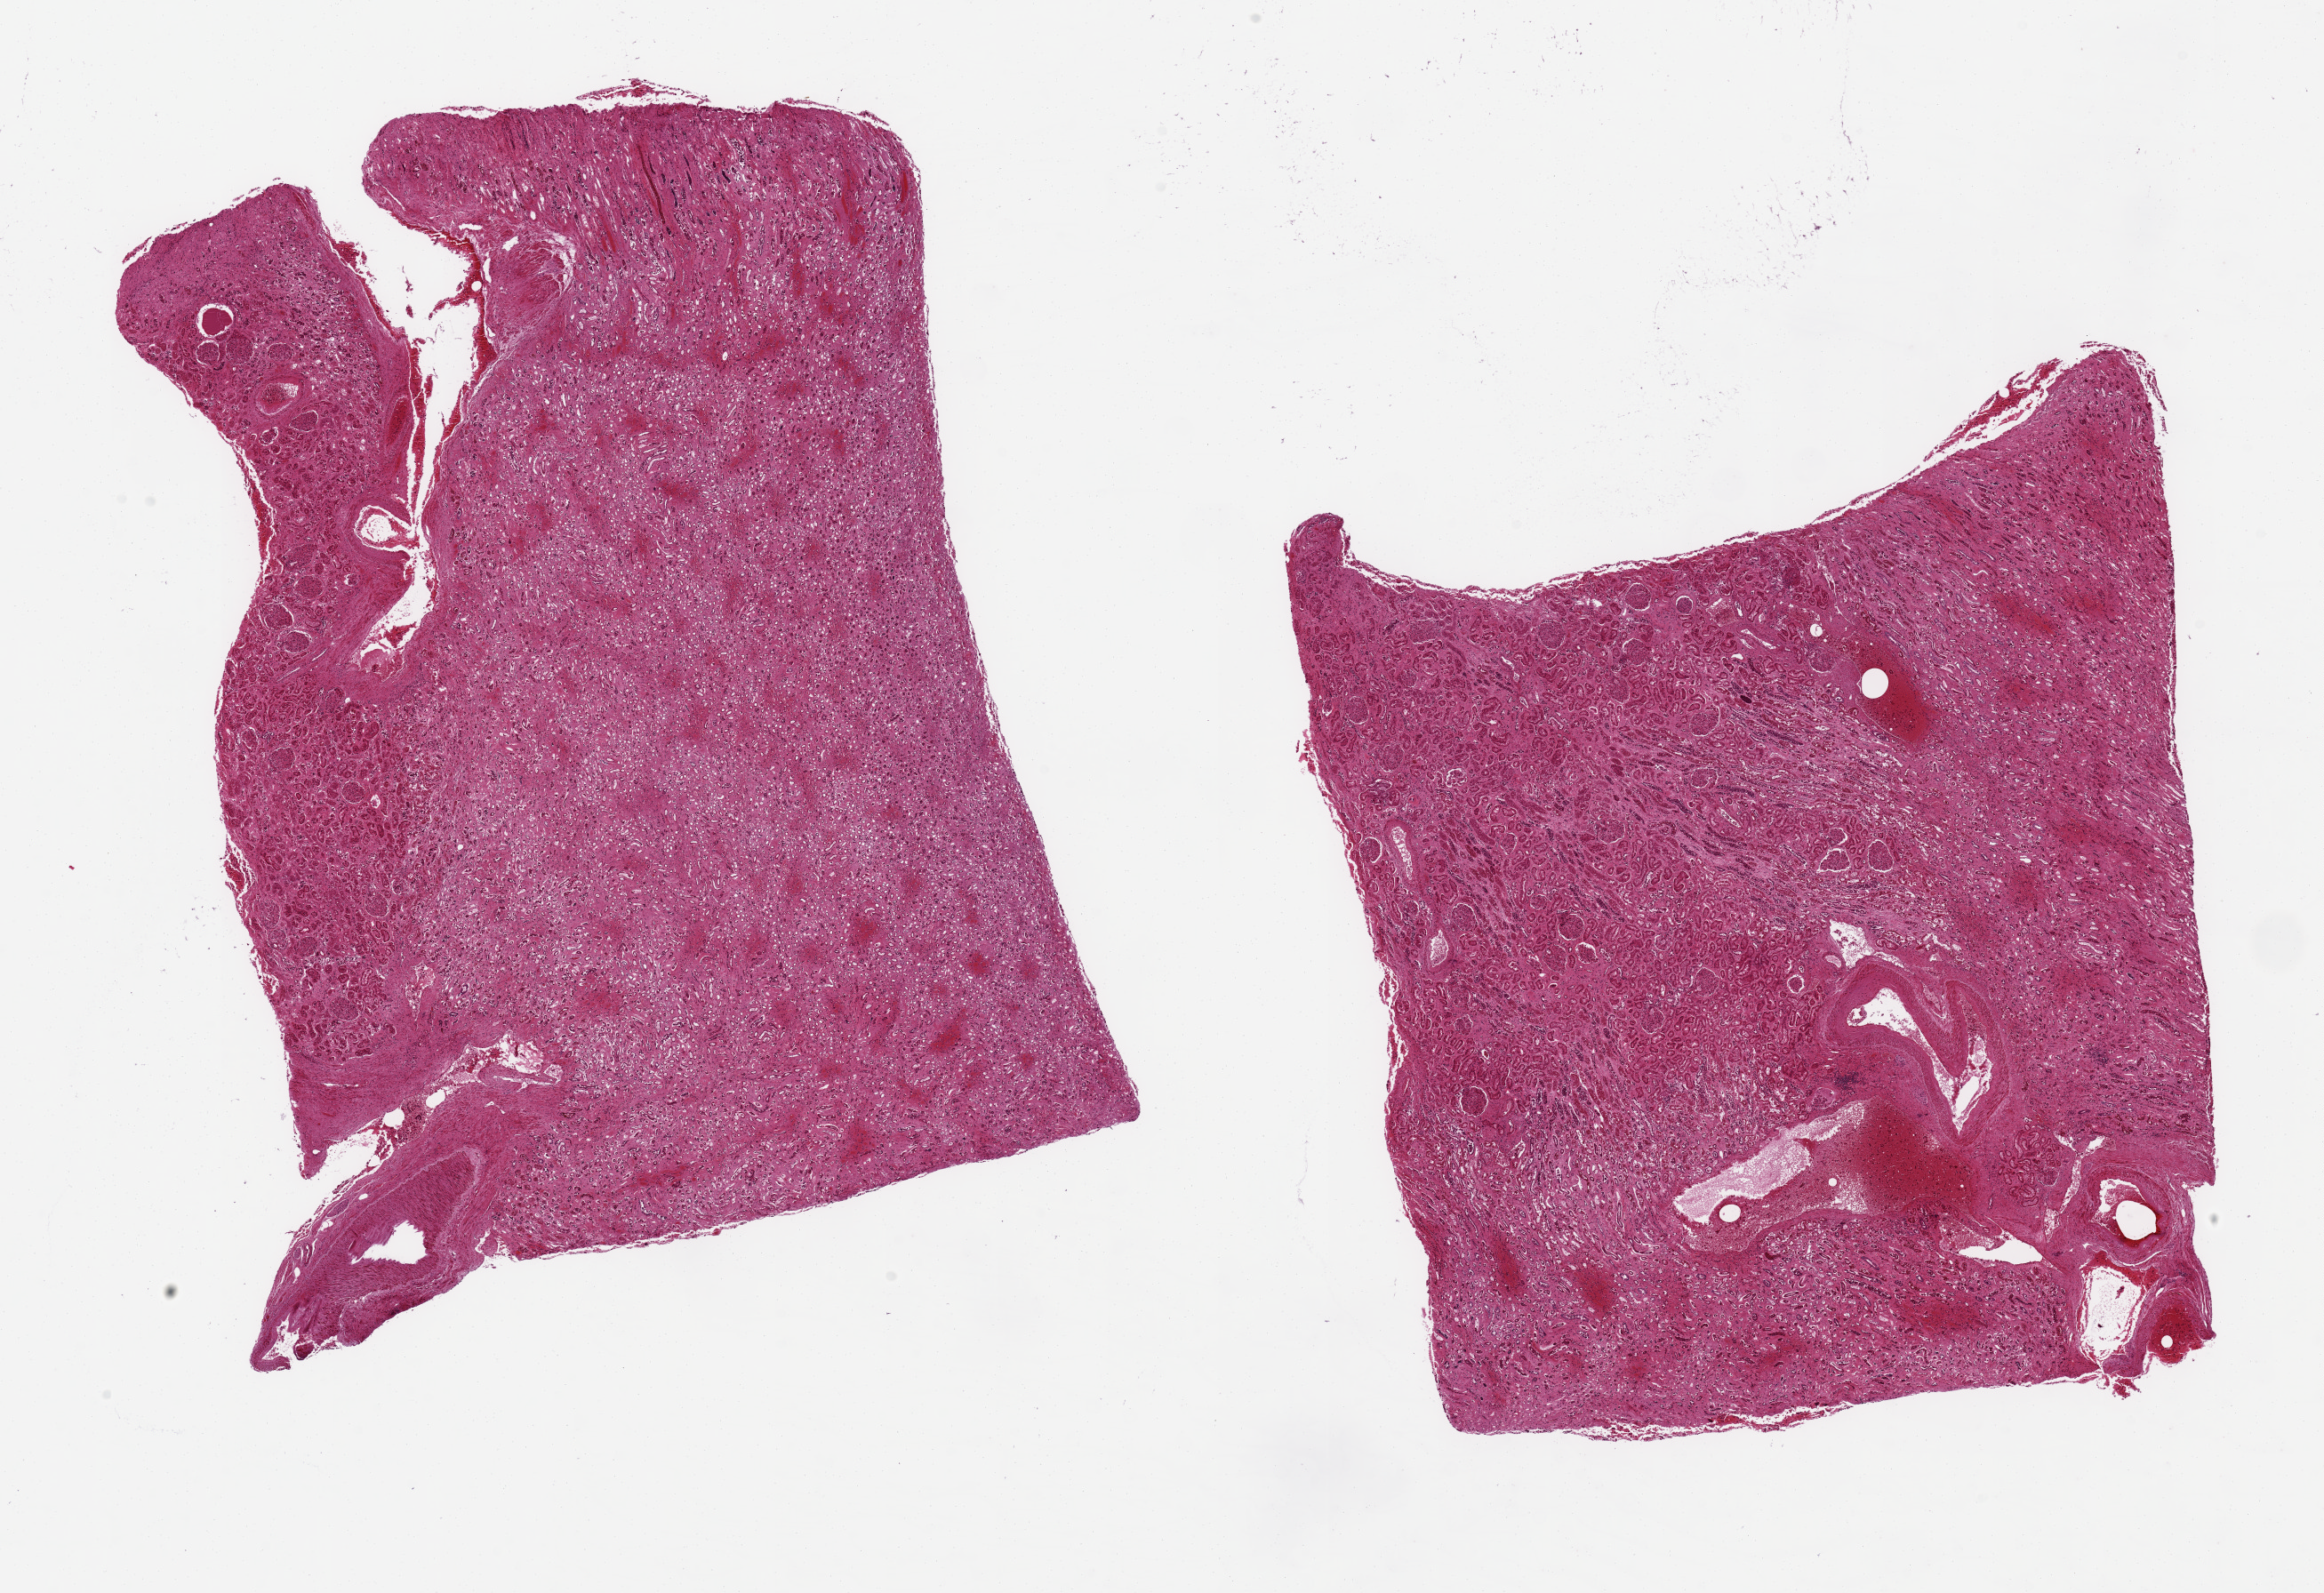
H&E whole-slide image, whole scanned area (about 20.7 x 14.2 mm, from a 20x scan) shown as a low-resolution overview. Male donor.
Specimen: PAXgene-fixed paraffin-embedded (PFPE) section; target tissue: renal medulla; tissue donor sample.